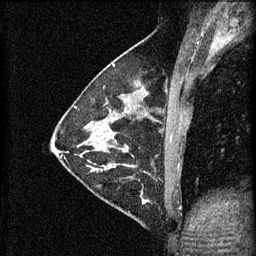
Breast MRI (dynamic contrast-enhanced), one sagittal slice. Position 23 of 60 along the scan axis. 3 images stored at this slice position (order not interpretable as contrast timing). 1.5 T. TE 4.2 ms, TR 11 ms. 2 mm slice thickness. 256 × 256 image matrix, field of view 180 × 180 mm. Patient: female, 29 years.
Outlined on this slice (semi-automatic segmentation, software-assisted and operator-edited):
- analysis volume of interest (the breast-tissue region the enhancement analysis was run in; not a lesion): bounding box [x1, y1, x2, y2] px = [105, 172, 171, 227]
- tumour enhancement mask (voxels above the 70 % enhancement threshold inside the analysis volume of interest): [143, 200, 149, 205]